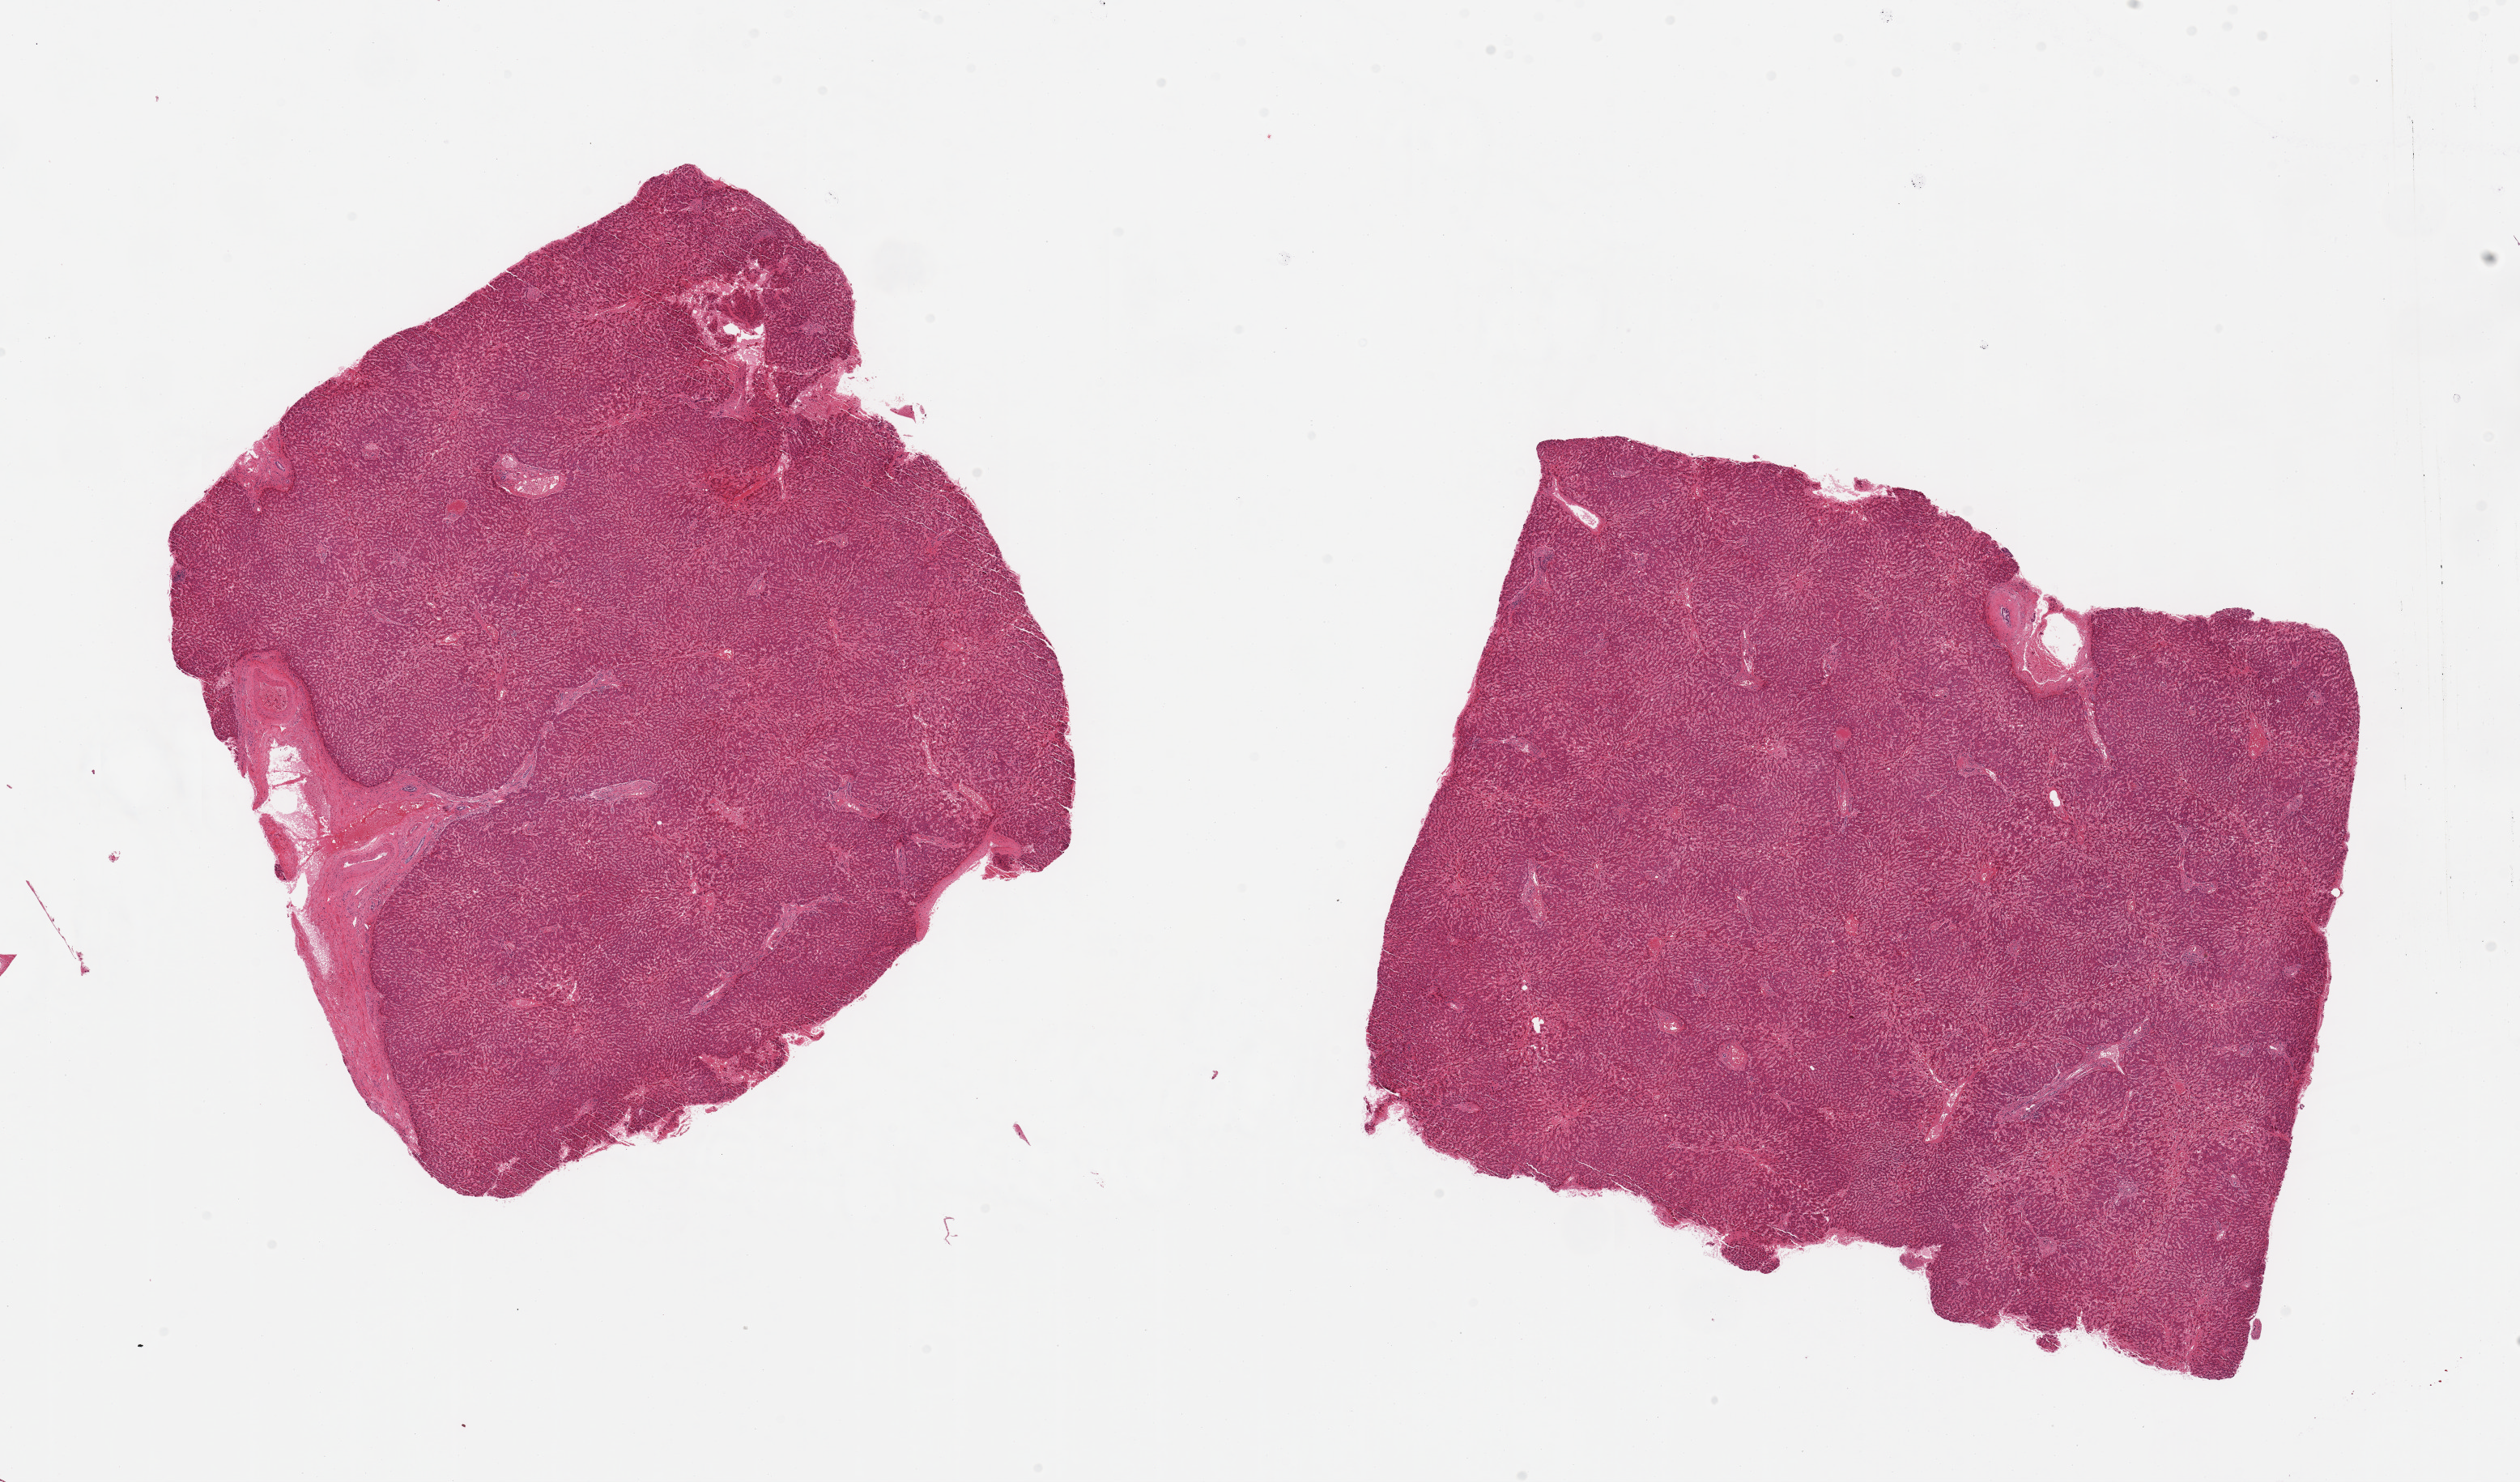
Digitized hematoxylin and eosin (H&E)-stained section, shown as a low-resolution overview of the whole scanned area (about 24.6 x 14.5 mm, from a 20x scan). PAXgene-fixed, paraffin-embedded tissue. Section of liver (target tissue). Tissue donor sample. Donor: male.
- reviewer comment on this tissue sample: 2 pieces, no steatosis, moderate congestion